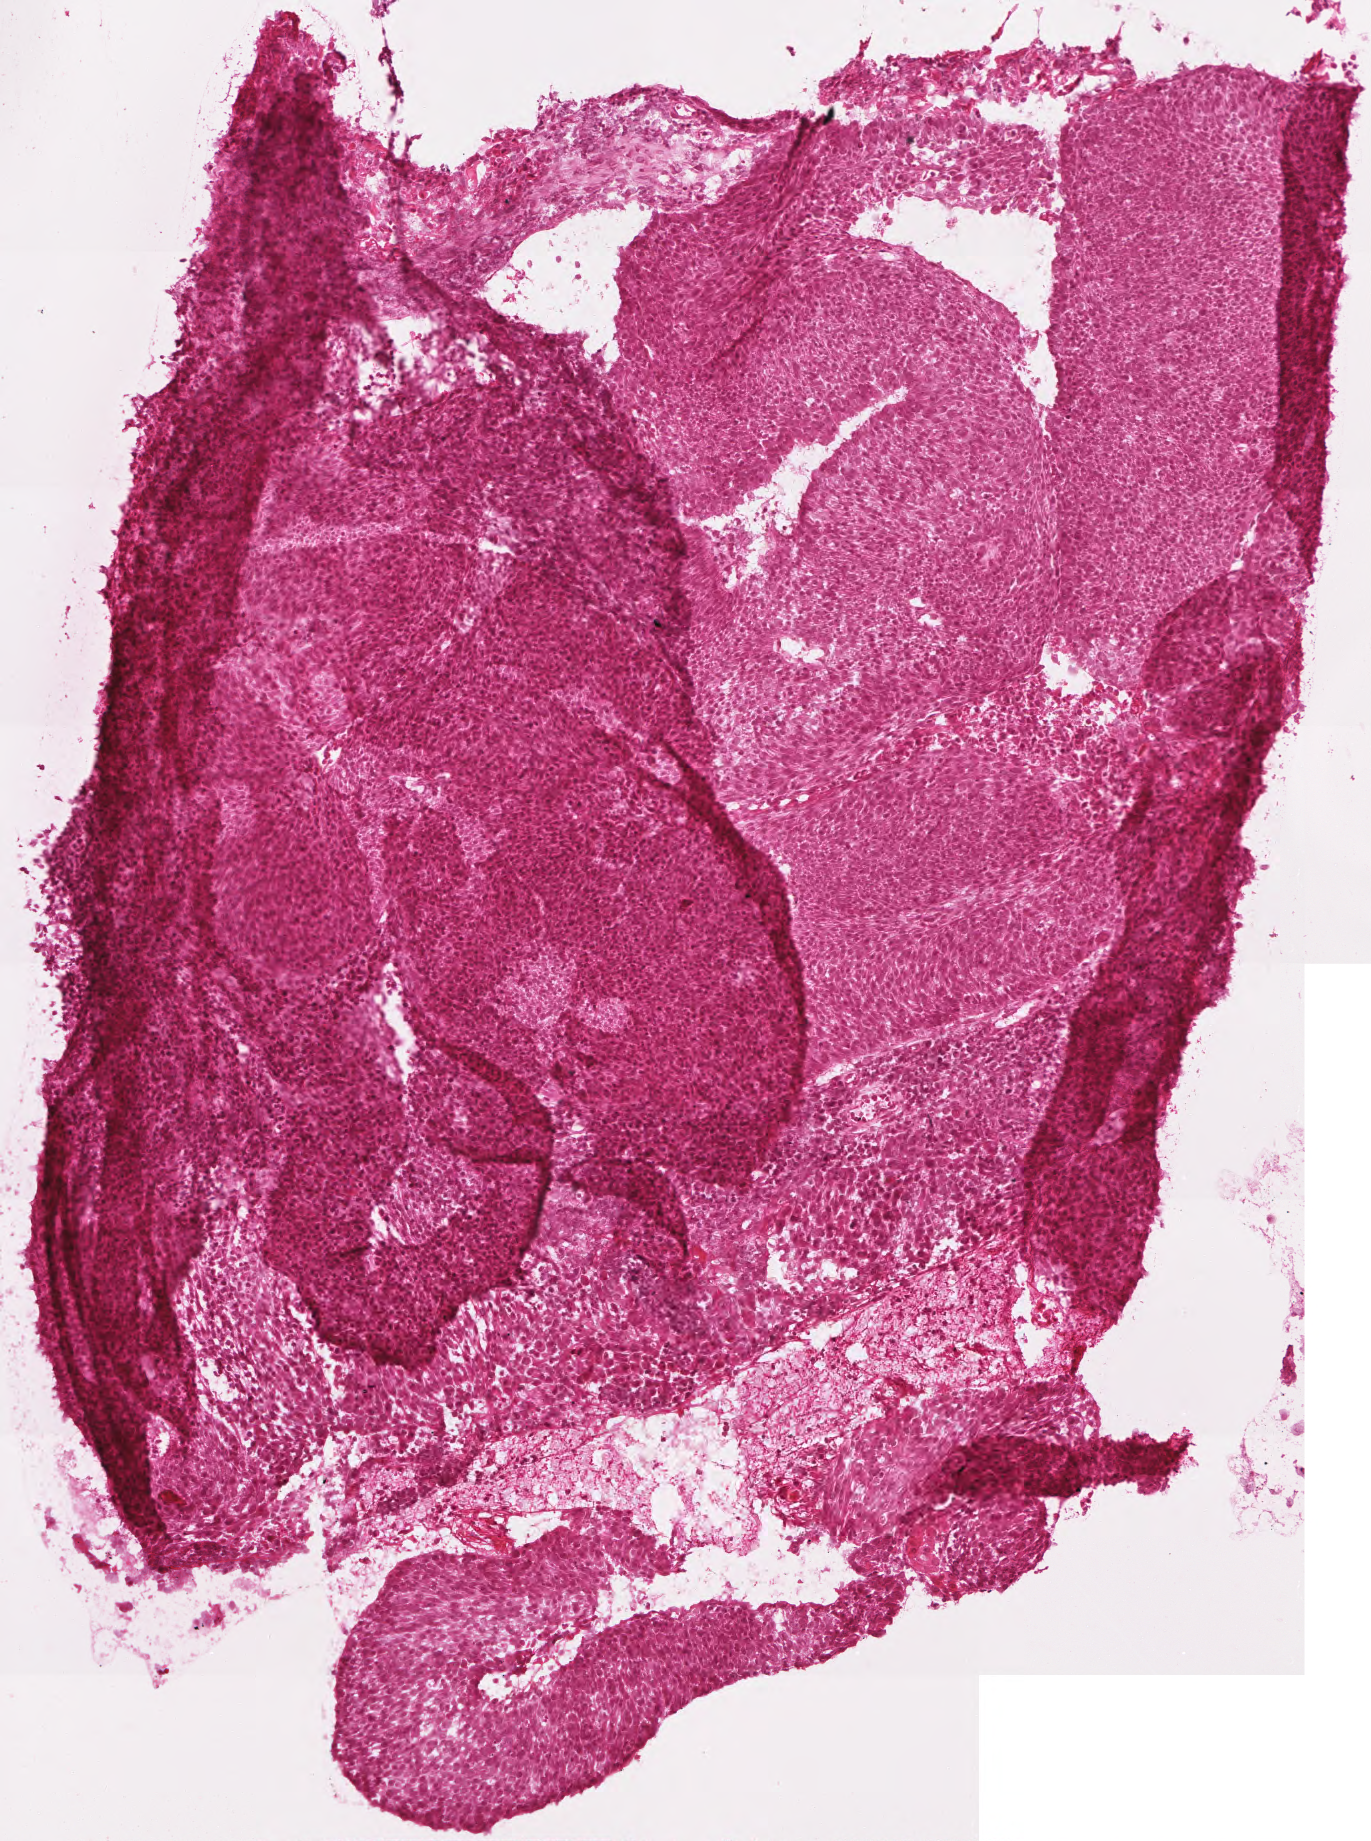
Digitized H&E tissue section (whole slide), low-resolution overview of the scanned area, about 2.7 x 3.7 mm; frozen section from the top of the tissue portion; head and neck, primary tumour sample. Patient: male, age at initial diagnosis 53 years. Histologic grade: G2 (moderately differentiated). Composition of this section per pathologist review: tumour cells 95%, tumour nuclei 95%, normal cells 0%, stromal cells 5%, necrosis 0%.
• histologic diagnosis: Squamous cell carcinoma, NOS (tonsil, NOS)